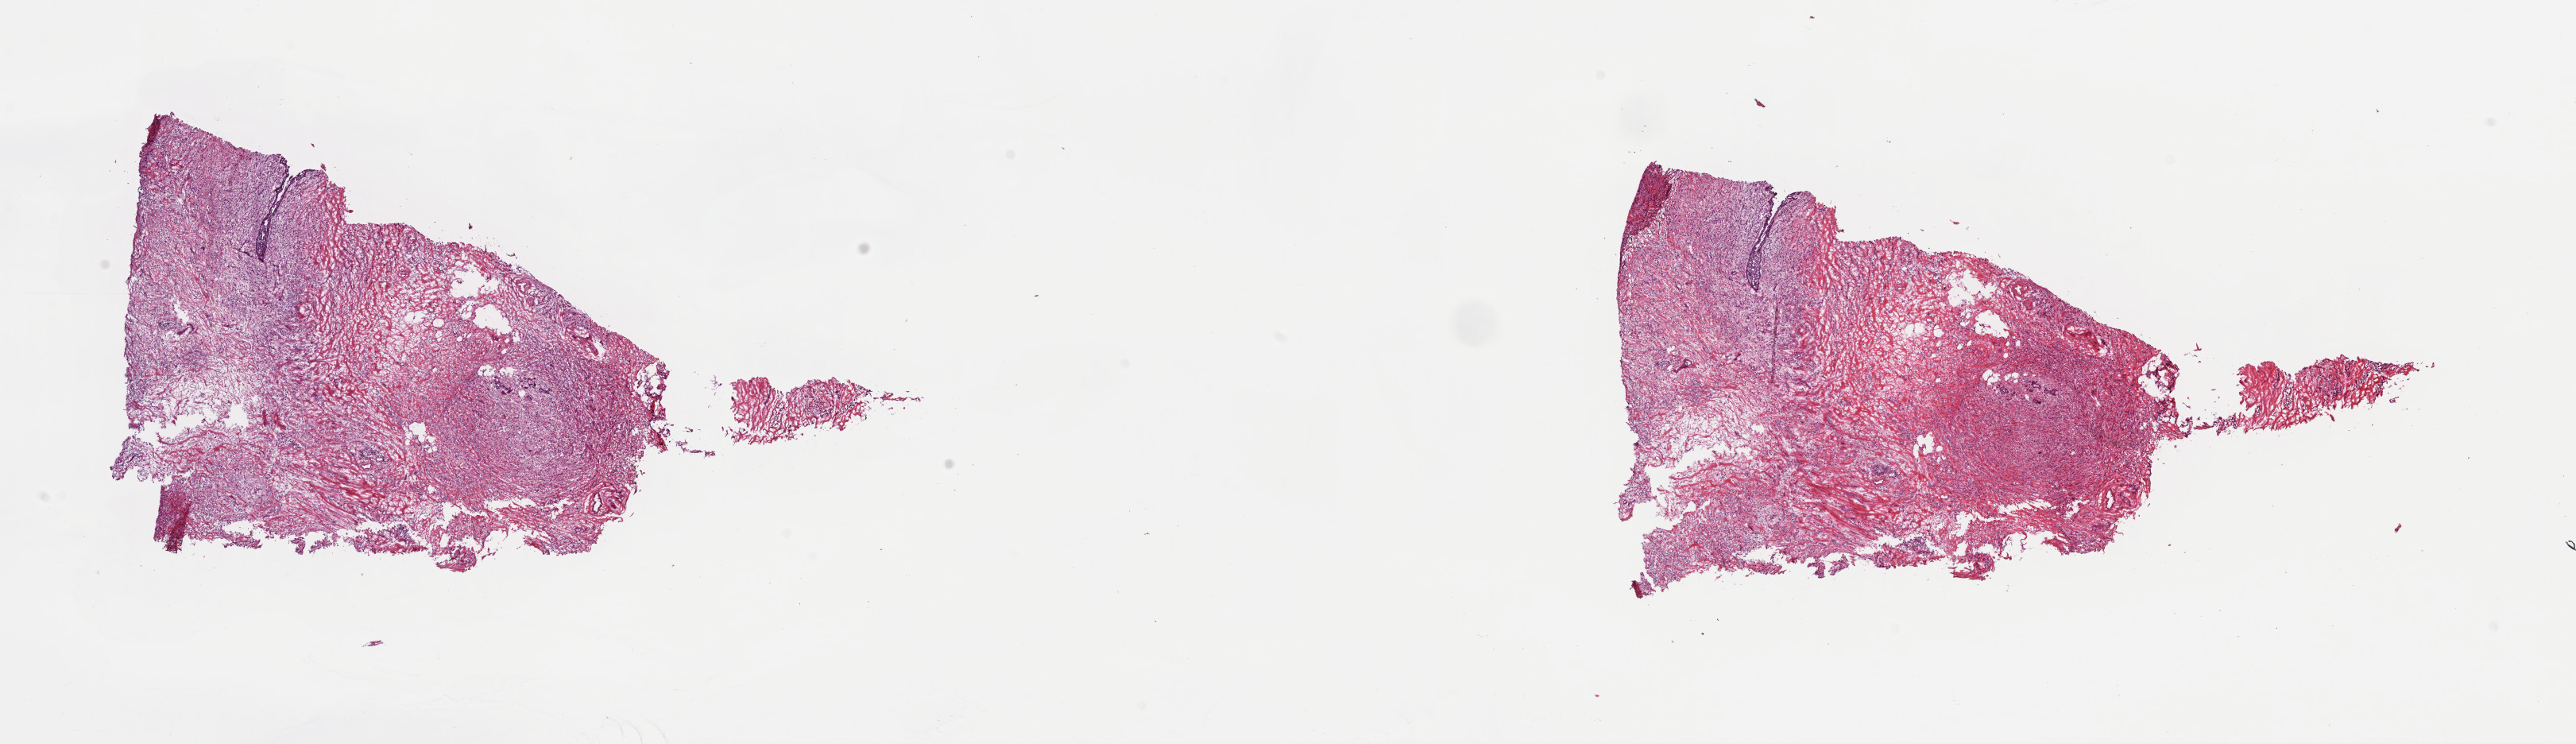
Digitized Hematoxylin and eosin (H&E) stained tissue section (whole slide), shown as a low-resolution overview of the whole scanned area (about 25.6 x 7.4 mm). Frozen section from the top of the tissue portion. Sample: primary tumour, breast. Female patient; age at initial diagnosis 46 years. Slide review estimates, as recorded: tumour cells 98%, tumour nuclei 85%, normal cells 2%, stromal cells 0%, necrosis 0%. Inflammatory infiltration, as recorded: lymphocyte infiltration 0%, monocyte infiltration 0%, neutrophil infiltration 0%.
AJCC pathologic stage: IIIC (7th edition). Diagnosis: Lobular carcinoma, NOS.